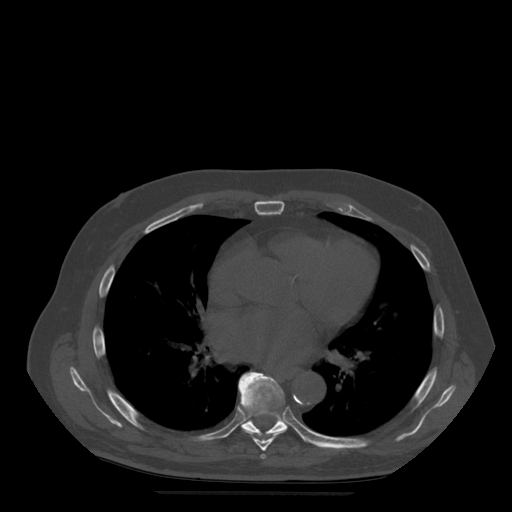
CT including the spine, one axial slice; slice 324 of 522 in the series (ordered by position); bone window (W 1800 / L 400 HU); 1.25 mm slice thickness; 512 × 512 image matrix, field of view 420 × 420 mm. Patient age 72 years. Case-level facts recorded for this patient, not image findings: primary cancer: prostate.
Outlined on this slice (semi-automatically segmented with operator editing):
- T6 vertebra: bounding box [x1, y1, x2, y2] px = [260, 454, 266, 459]
- T7 vertebra: [239, 373, 288, 451]
- T8 vertebra: [239, 372, 309, 443]